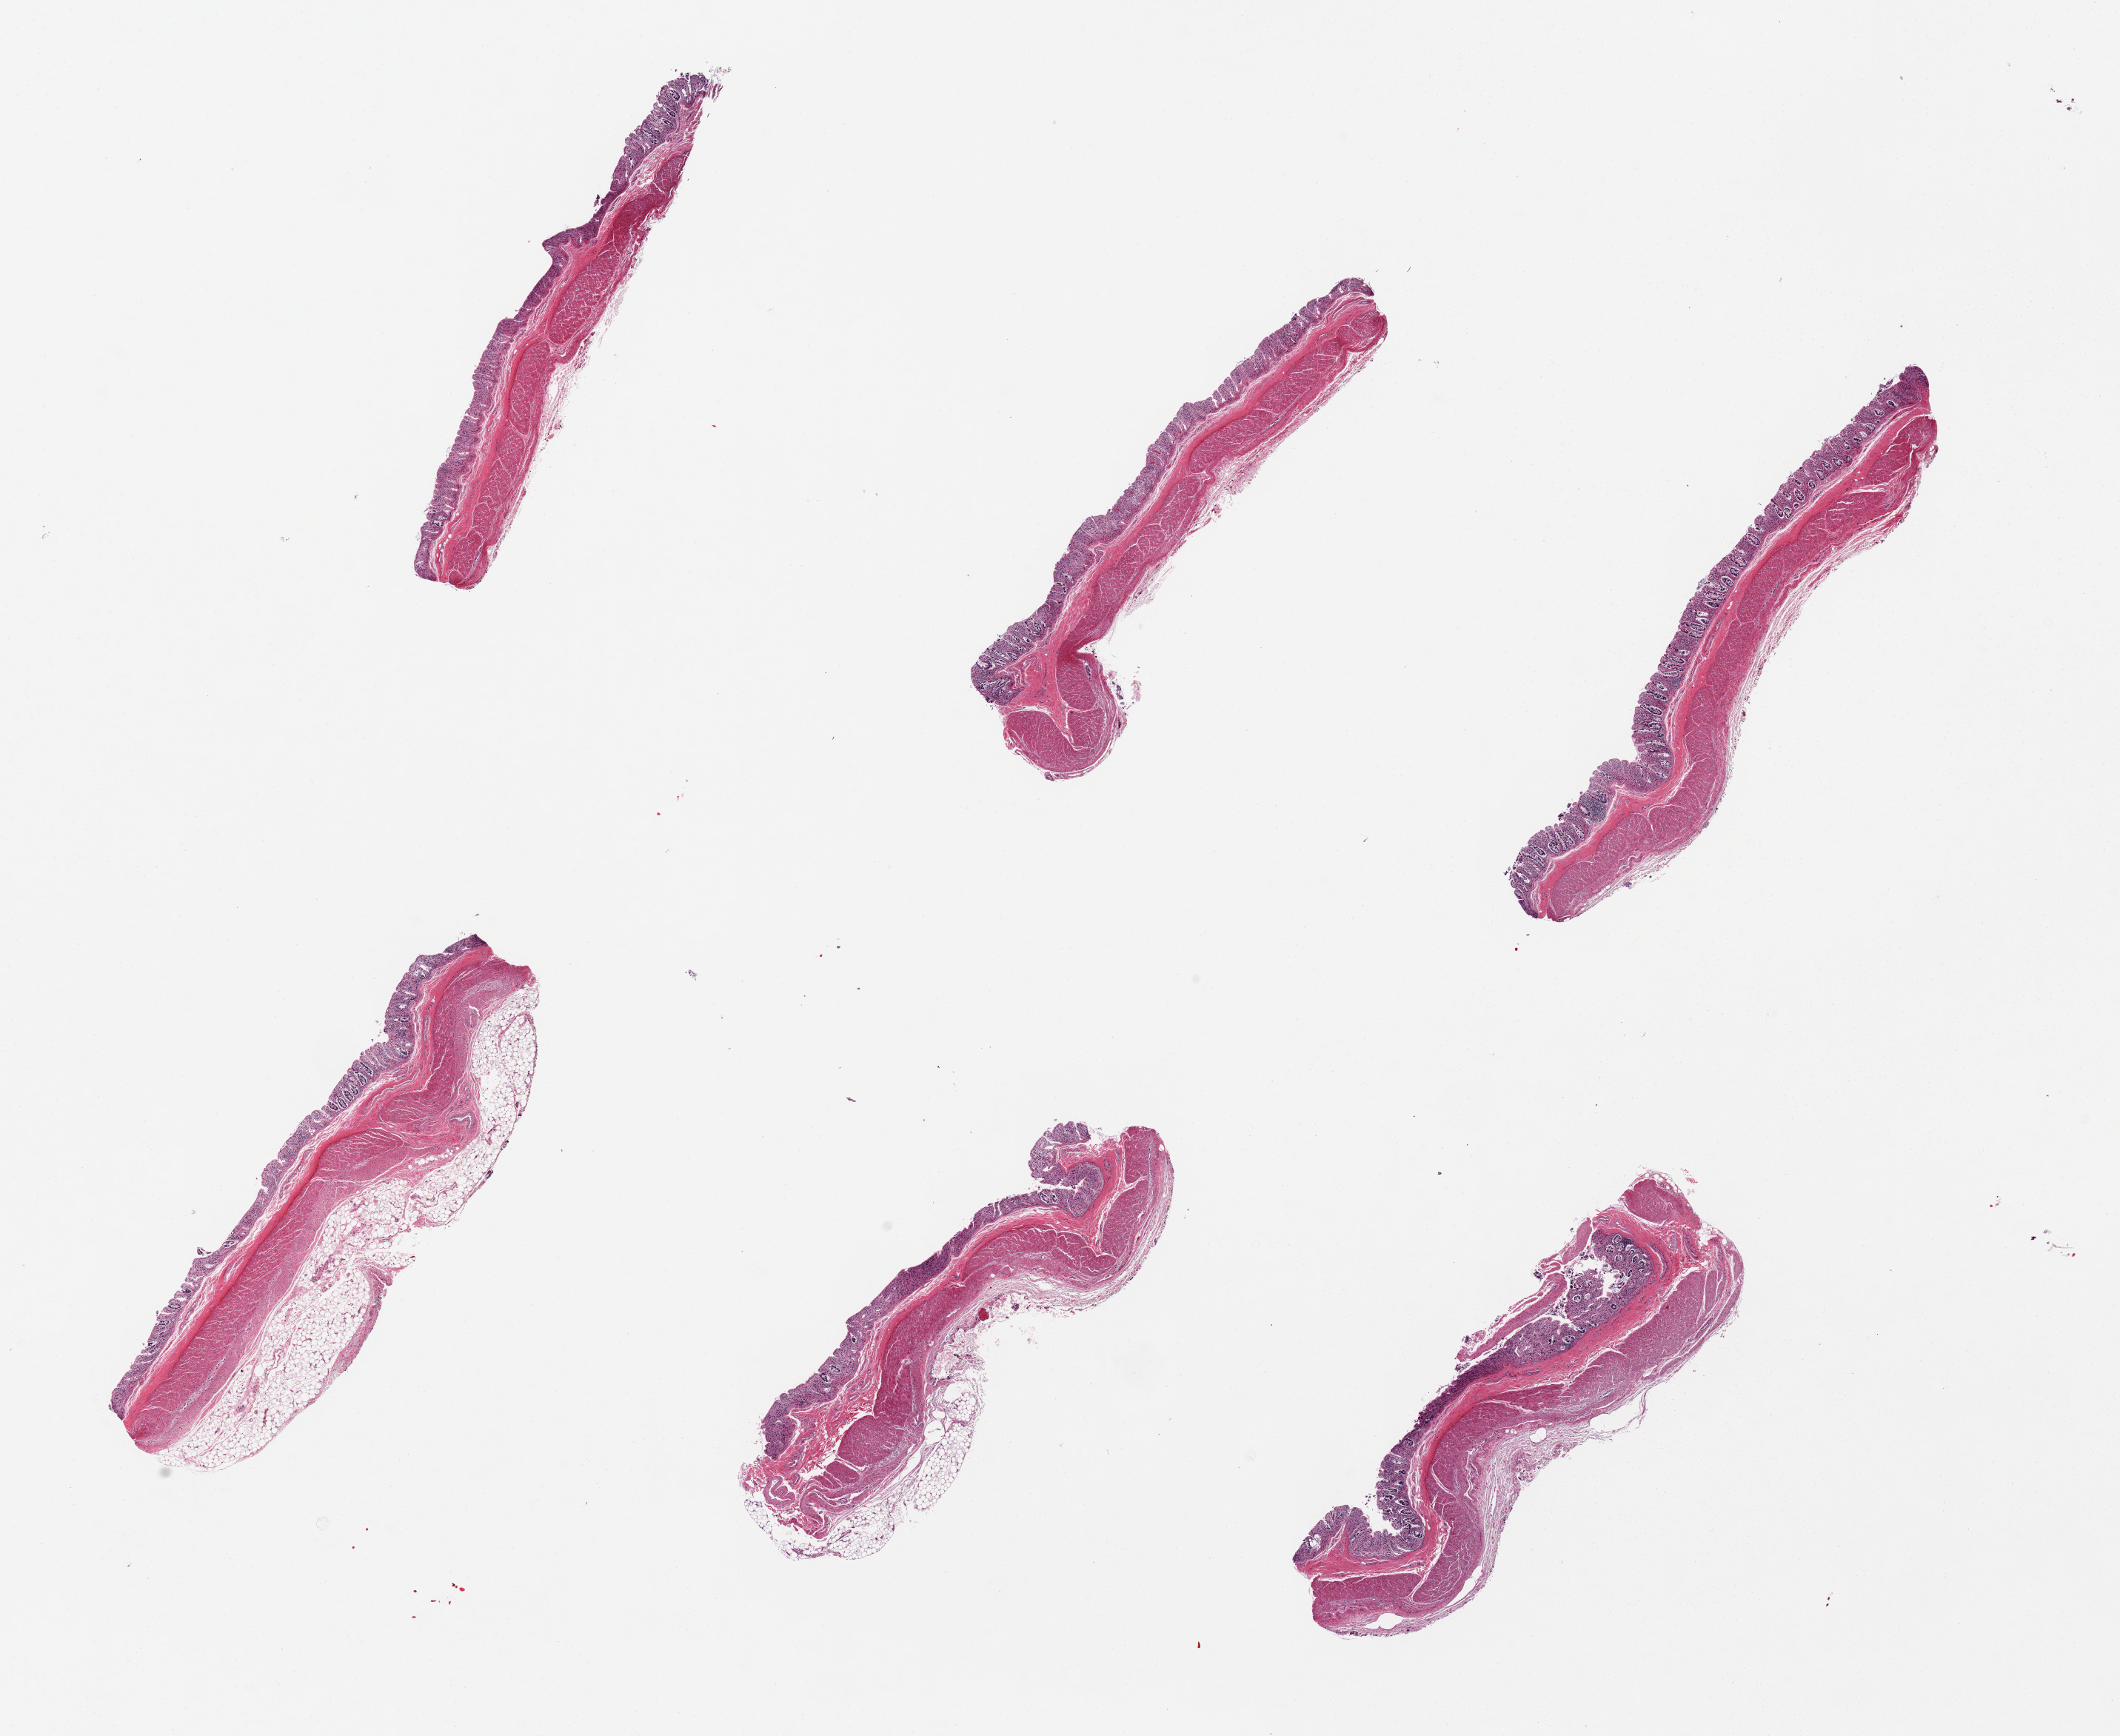
H&E whole-slide image, a low-resolution overview of the entire scanned area, about 22.6 x 18.5 mm; PAXgene-fixed paraffin-embedded (PFPE) section; section of transverse colon (target tissue); tissue donor sample. Donor: male.
Reviewer comment on this tissue sample: 6 pieces. Full thickness with 3 having pericolonic adipose up to 1 mm. Mucosa=3; muscle=1.